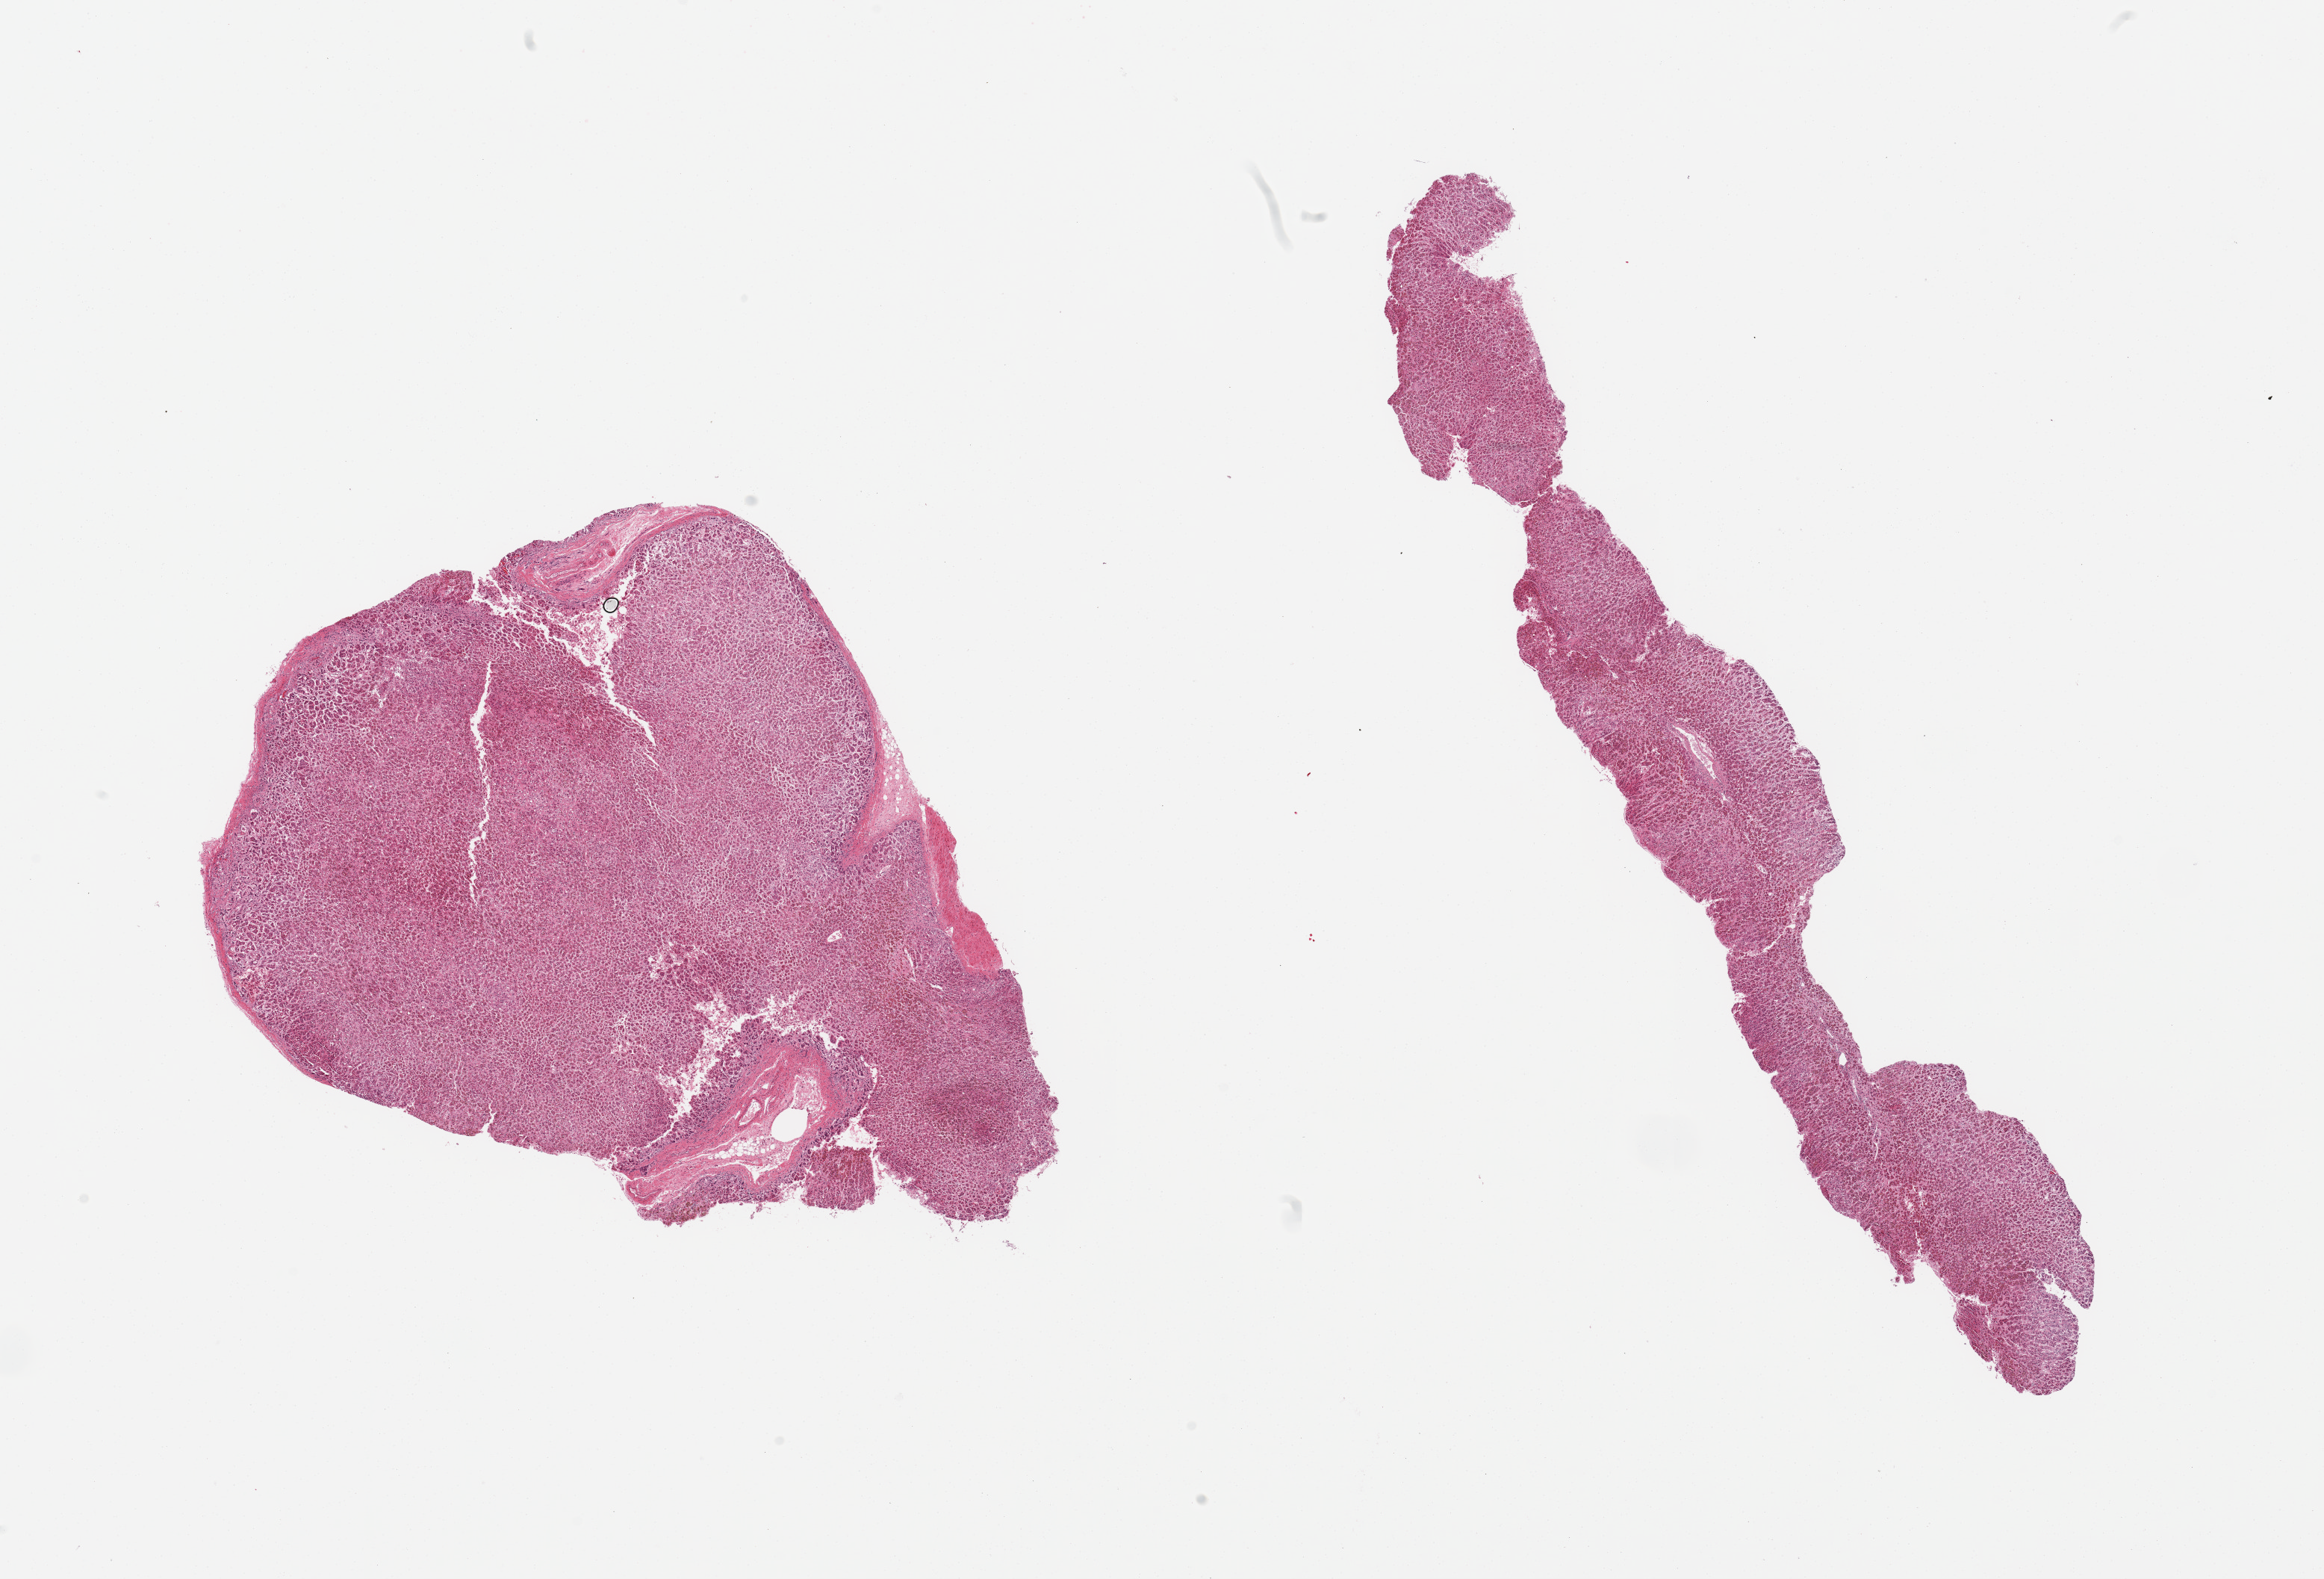
Digitized haematoxylin and eosin-stained section, a low-resolution overview of the entire scanned area, about 24.6 x 16.7 mm (acquisition: 20x scan); PAXgene-fixed, paraffin-embedded tissue; target tissue: adrenal gland; tissue donor sample. Donor: male.
Reviewer comment on this tissue sample: 2 pieces.